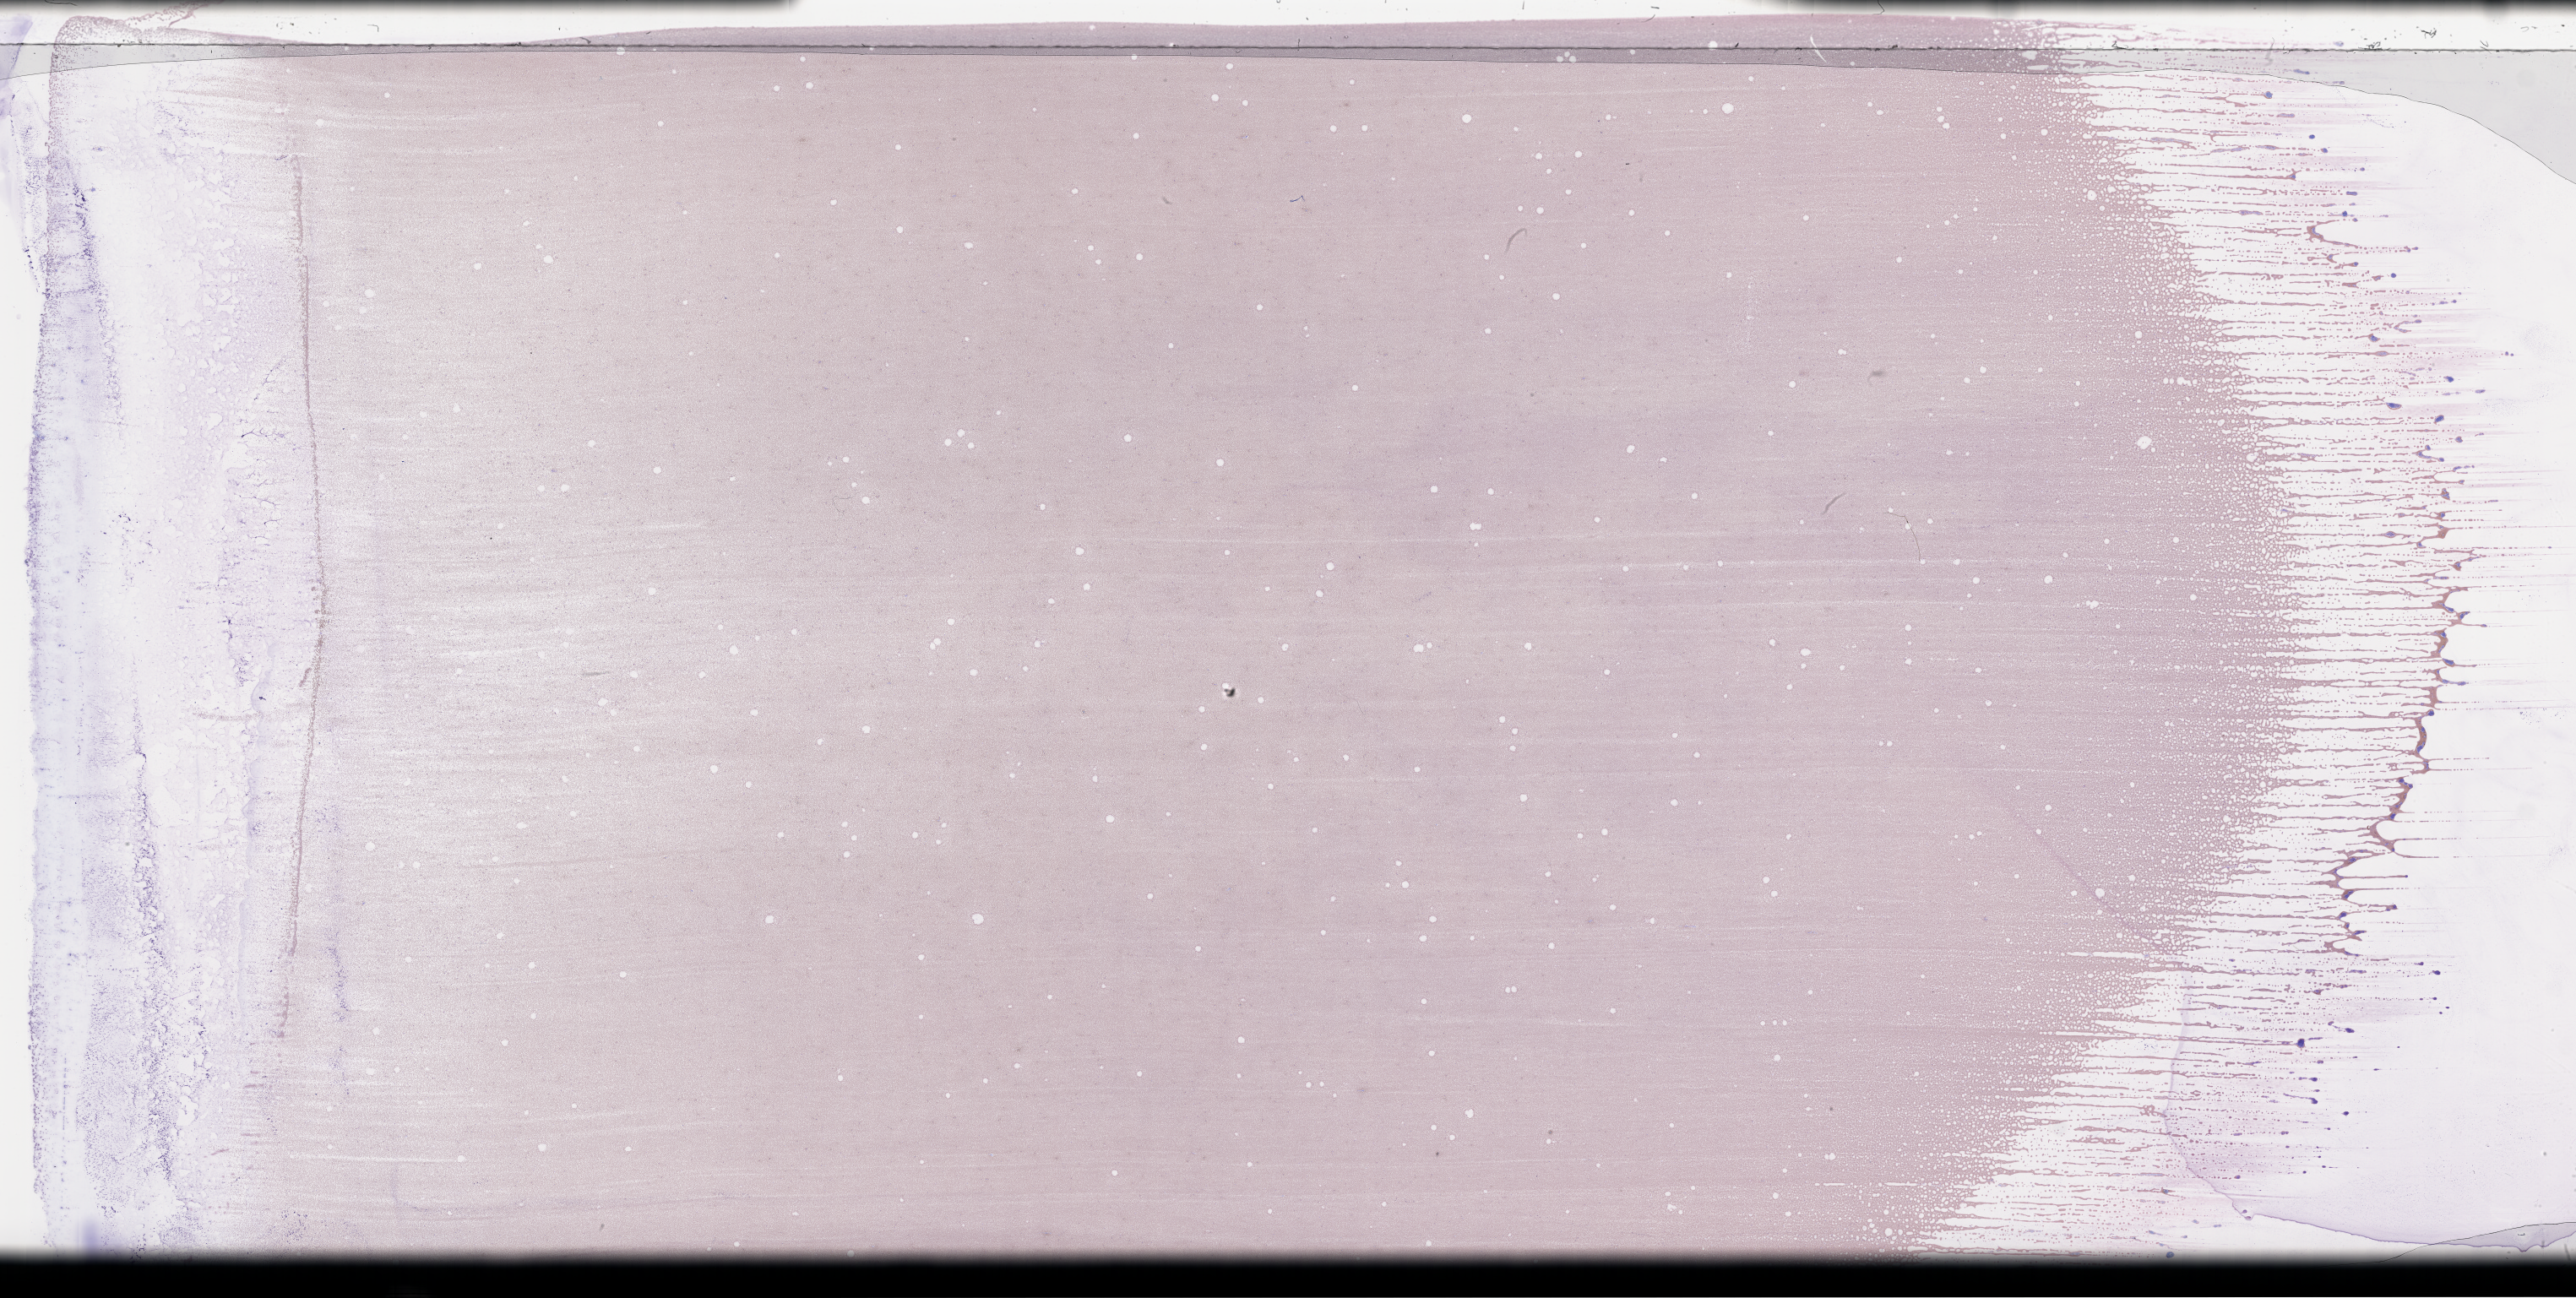
Whole-slide image of a whole blood smear, Wright–Giemsa stain, low-resolution overview of the scanned area, about 49.3 x 24.8 mm, collected on treatment. Male patient.
Patient diagnosis: Plasma Cell Myeloma.